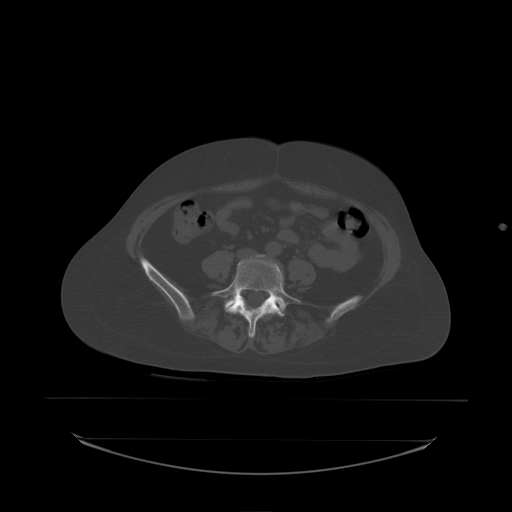
CT including the spine, one axial slice. Position 40 of 242 along the scan axis. Bone window (W 1800 / L 400 HU). 2.5 mm slice thickness. 512 × 512 image matrix, field of view 500 × 500 mm. Female patient, age 53 years. From the clinical record (not read from this slice): primary cancer: lung; vertebrae with lytic lesions (as recorded): T7, L1.
Annotated regions visible in this slice (semi-automatic segmentation, software-assisted and operator-edited):
- L5 vertebra: bounding box (x1, y1, x2, y2) in pixels: (214, 255, 301, 338)